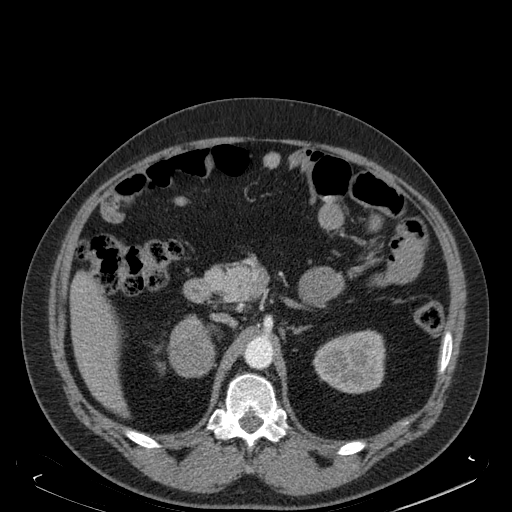
Contrast-enhanced abdominal CT, one axial slice. Soft-tissue window (W 400 / L 40 HU). 1.5 mm slice thickness. 512 × 512 image matrix, field of view 405 × 405 mm. Male patient. Case-level facts recorded for this patient, not image findings: diagnosis: adrenocortical carcinoma; tumour side: right adrenal; tumour size at pathology: 7.5 cm.
Annotated regions visible in this slice (semi-automatic segmentation, software-assisted and operator-edited):
- mass: bounding box [x1, y1, x2, y2] px = [170, 315, 213, 376]